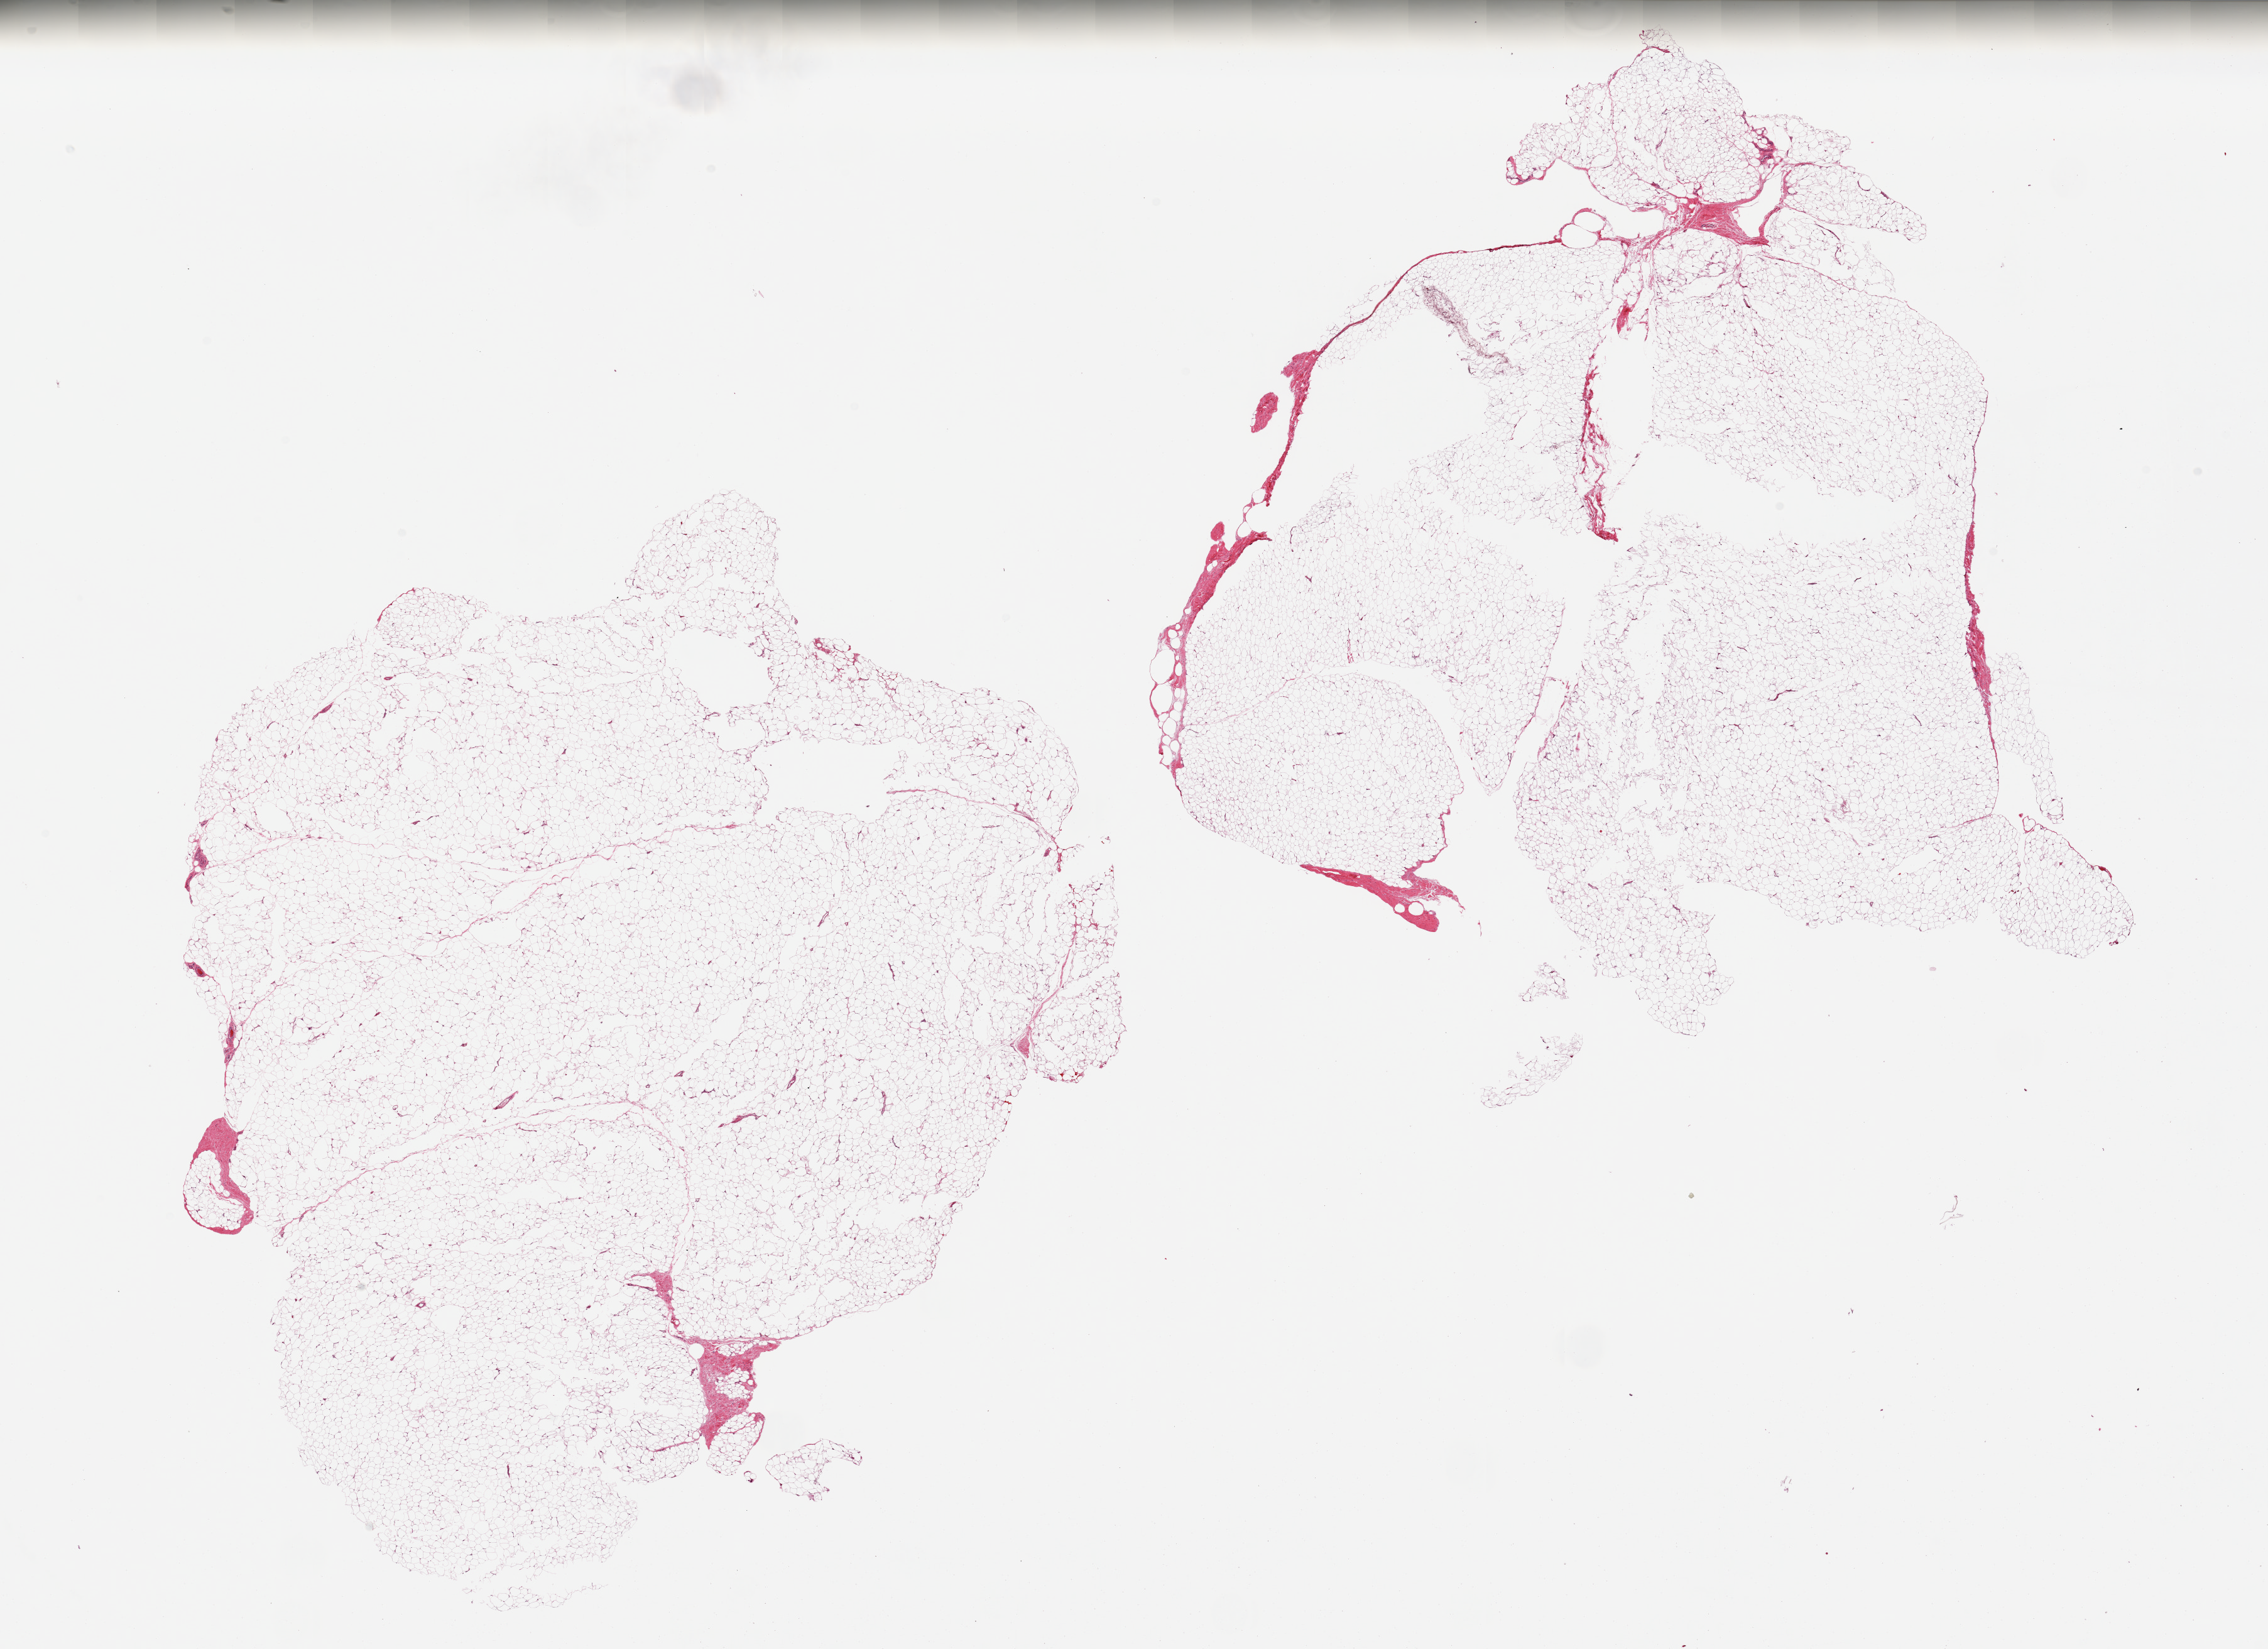
Digitized haematoxylin and eosin-stained section, brightfield, low-resolution overview of the scanned area, about 28.5 x 20.8 mm, PAXgene-fixed, paraffin-embedded tissue, section of adipose tissue (target tissue), donor tissue sample. Donor: female.
* pathologist's review note for this sample: 2 pieces. A few central artifacts